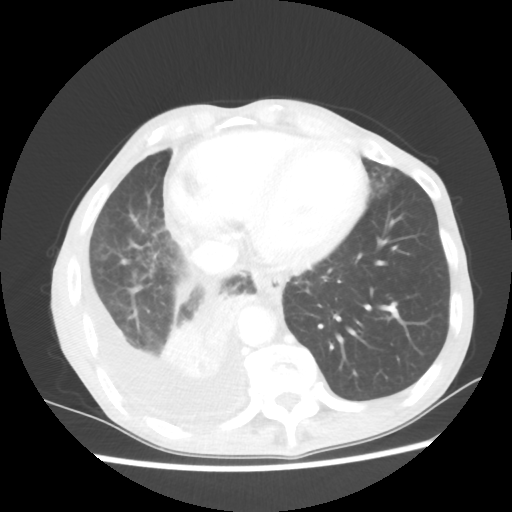
Chest CT, one axial slice. Position 17 of 60 along the scan axis. 80 kVp. Lung window (W 1500 / L -600 HU). 5 mm slice thickness. 512 × 512 image matrix, field of view 335 × 335 mm. Male patient, age 76 years. Case-level facts recorded for this patient, not image findings: clinical TNM (as recorded): T3 N3 M1a; histopathological grade: G3.
Outlined on this slice (rectangle marked by the reading radiologist):
- lung tumour (recorded histology: squamous cell carcinoma): bounding box <158,278,258,385> (left, top, right, bottom; pixels)